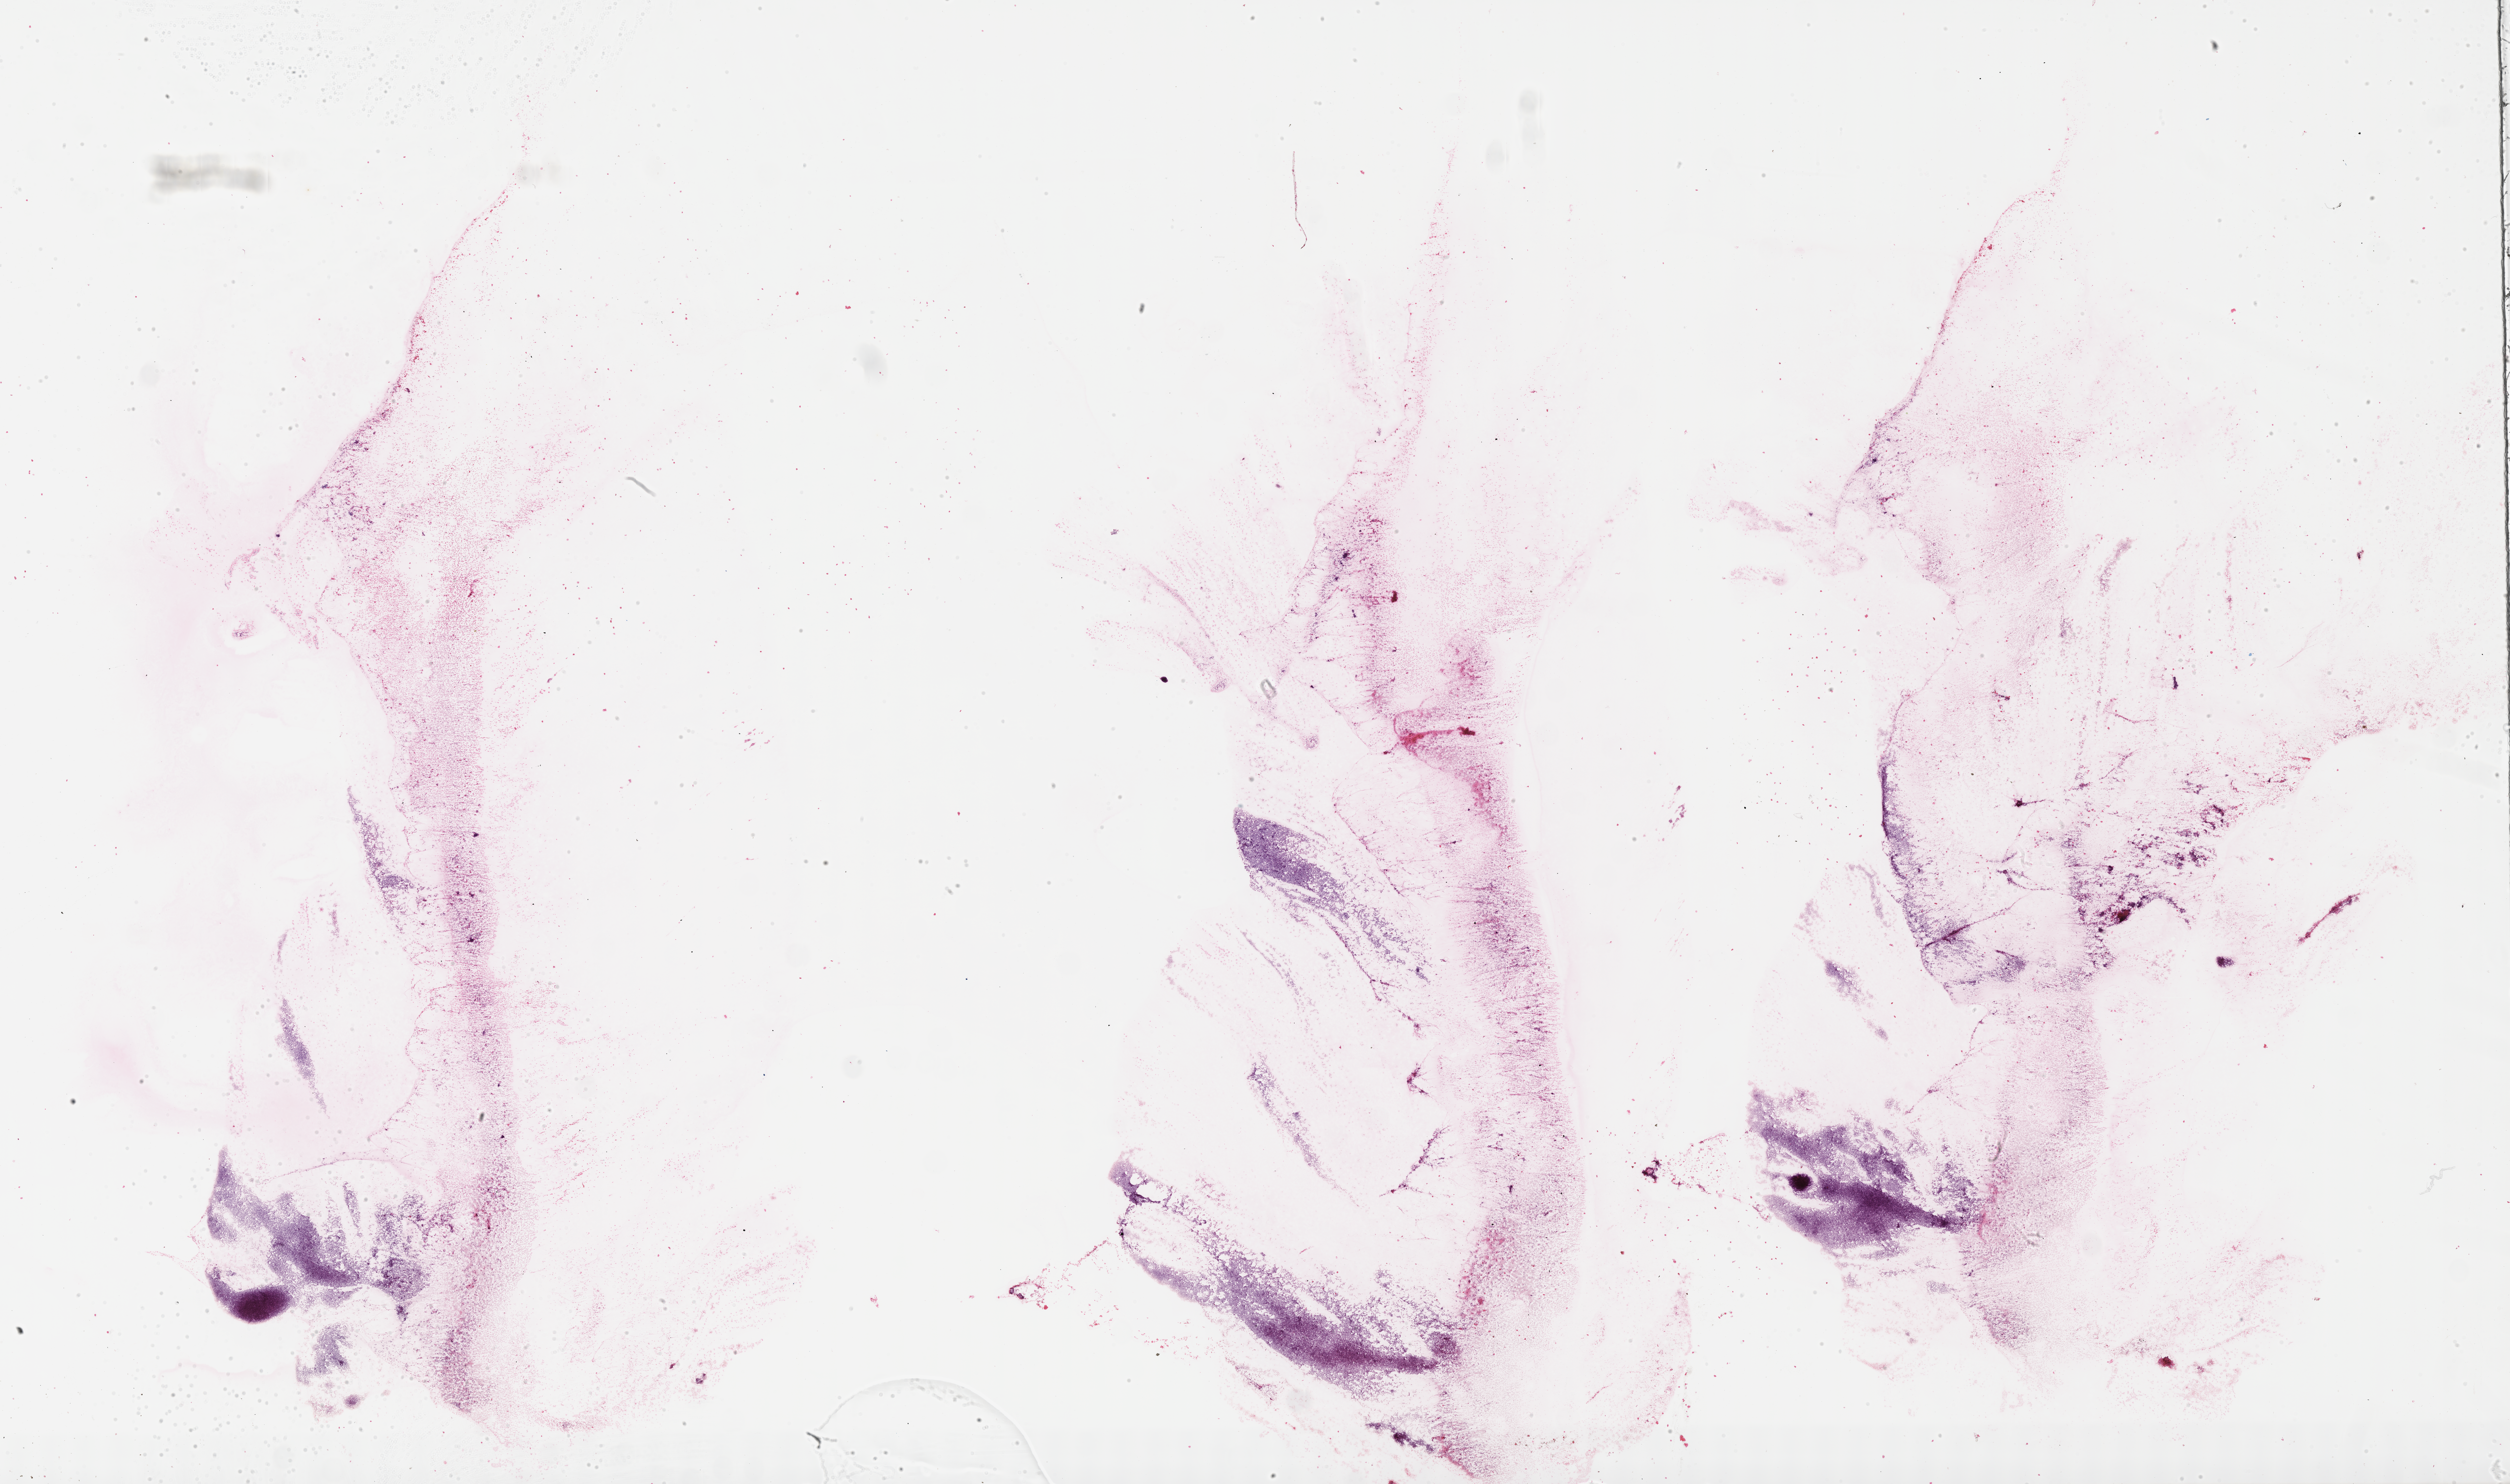
Digitized H&E-stained section of tumor tissue — low-resolution overview of the scanned area, about 37.7 x 22.3 mm, formalin-fixed, paraffin-embedded (FFPE) tissue, sample anatomic site: chest. Female patient, age at diagnosis 13.6 years.
Diagnosis: rhabdomyosarcoma; histological classification: alveolar rhabdomyosarcoma. Stage (as recorded): 4. Metastatic status at presentation (as recorded): metastatic (confirmed).